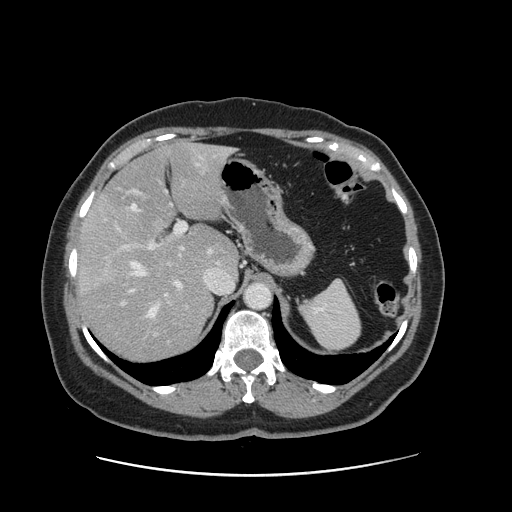
Contrast-enhanced abdominal CT, one axial slice; position 103 of 161 along the scan axis; intravenous contrast given; soft-tissue window (W 400 / L 40 HU); 2.5 mm slice thickness; 512 × 512 image matrix, field of view 398 × 398 mm. Female patient, age 62 years. Case-level facts recorded for this patient, not image findings: diagnosis: colorectal cancer liver metastases, imaged before liver resection; multiple liver metastases: no; largest metastasis: 2.5 cm.
Annotated regions visible in this slice (expert manual segmentation):
- hepatic veins: bounding box (x1, y1, x2, y2) in pixels: (130, 164, 233, 318)
- liver: (80, 144, 237, 361)
- planned liver remnant (the part of the liver to remain after resection): (102, 144, 237, 273)
- portal vein (with intrahepatic branches): (120, 170, 203, 336)
- liver metastasis: (117, 277, 130, 287)